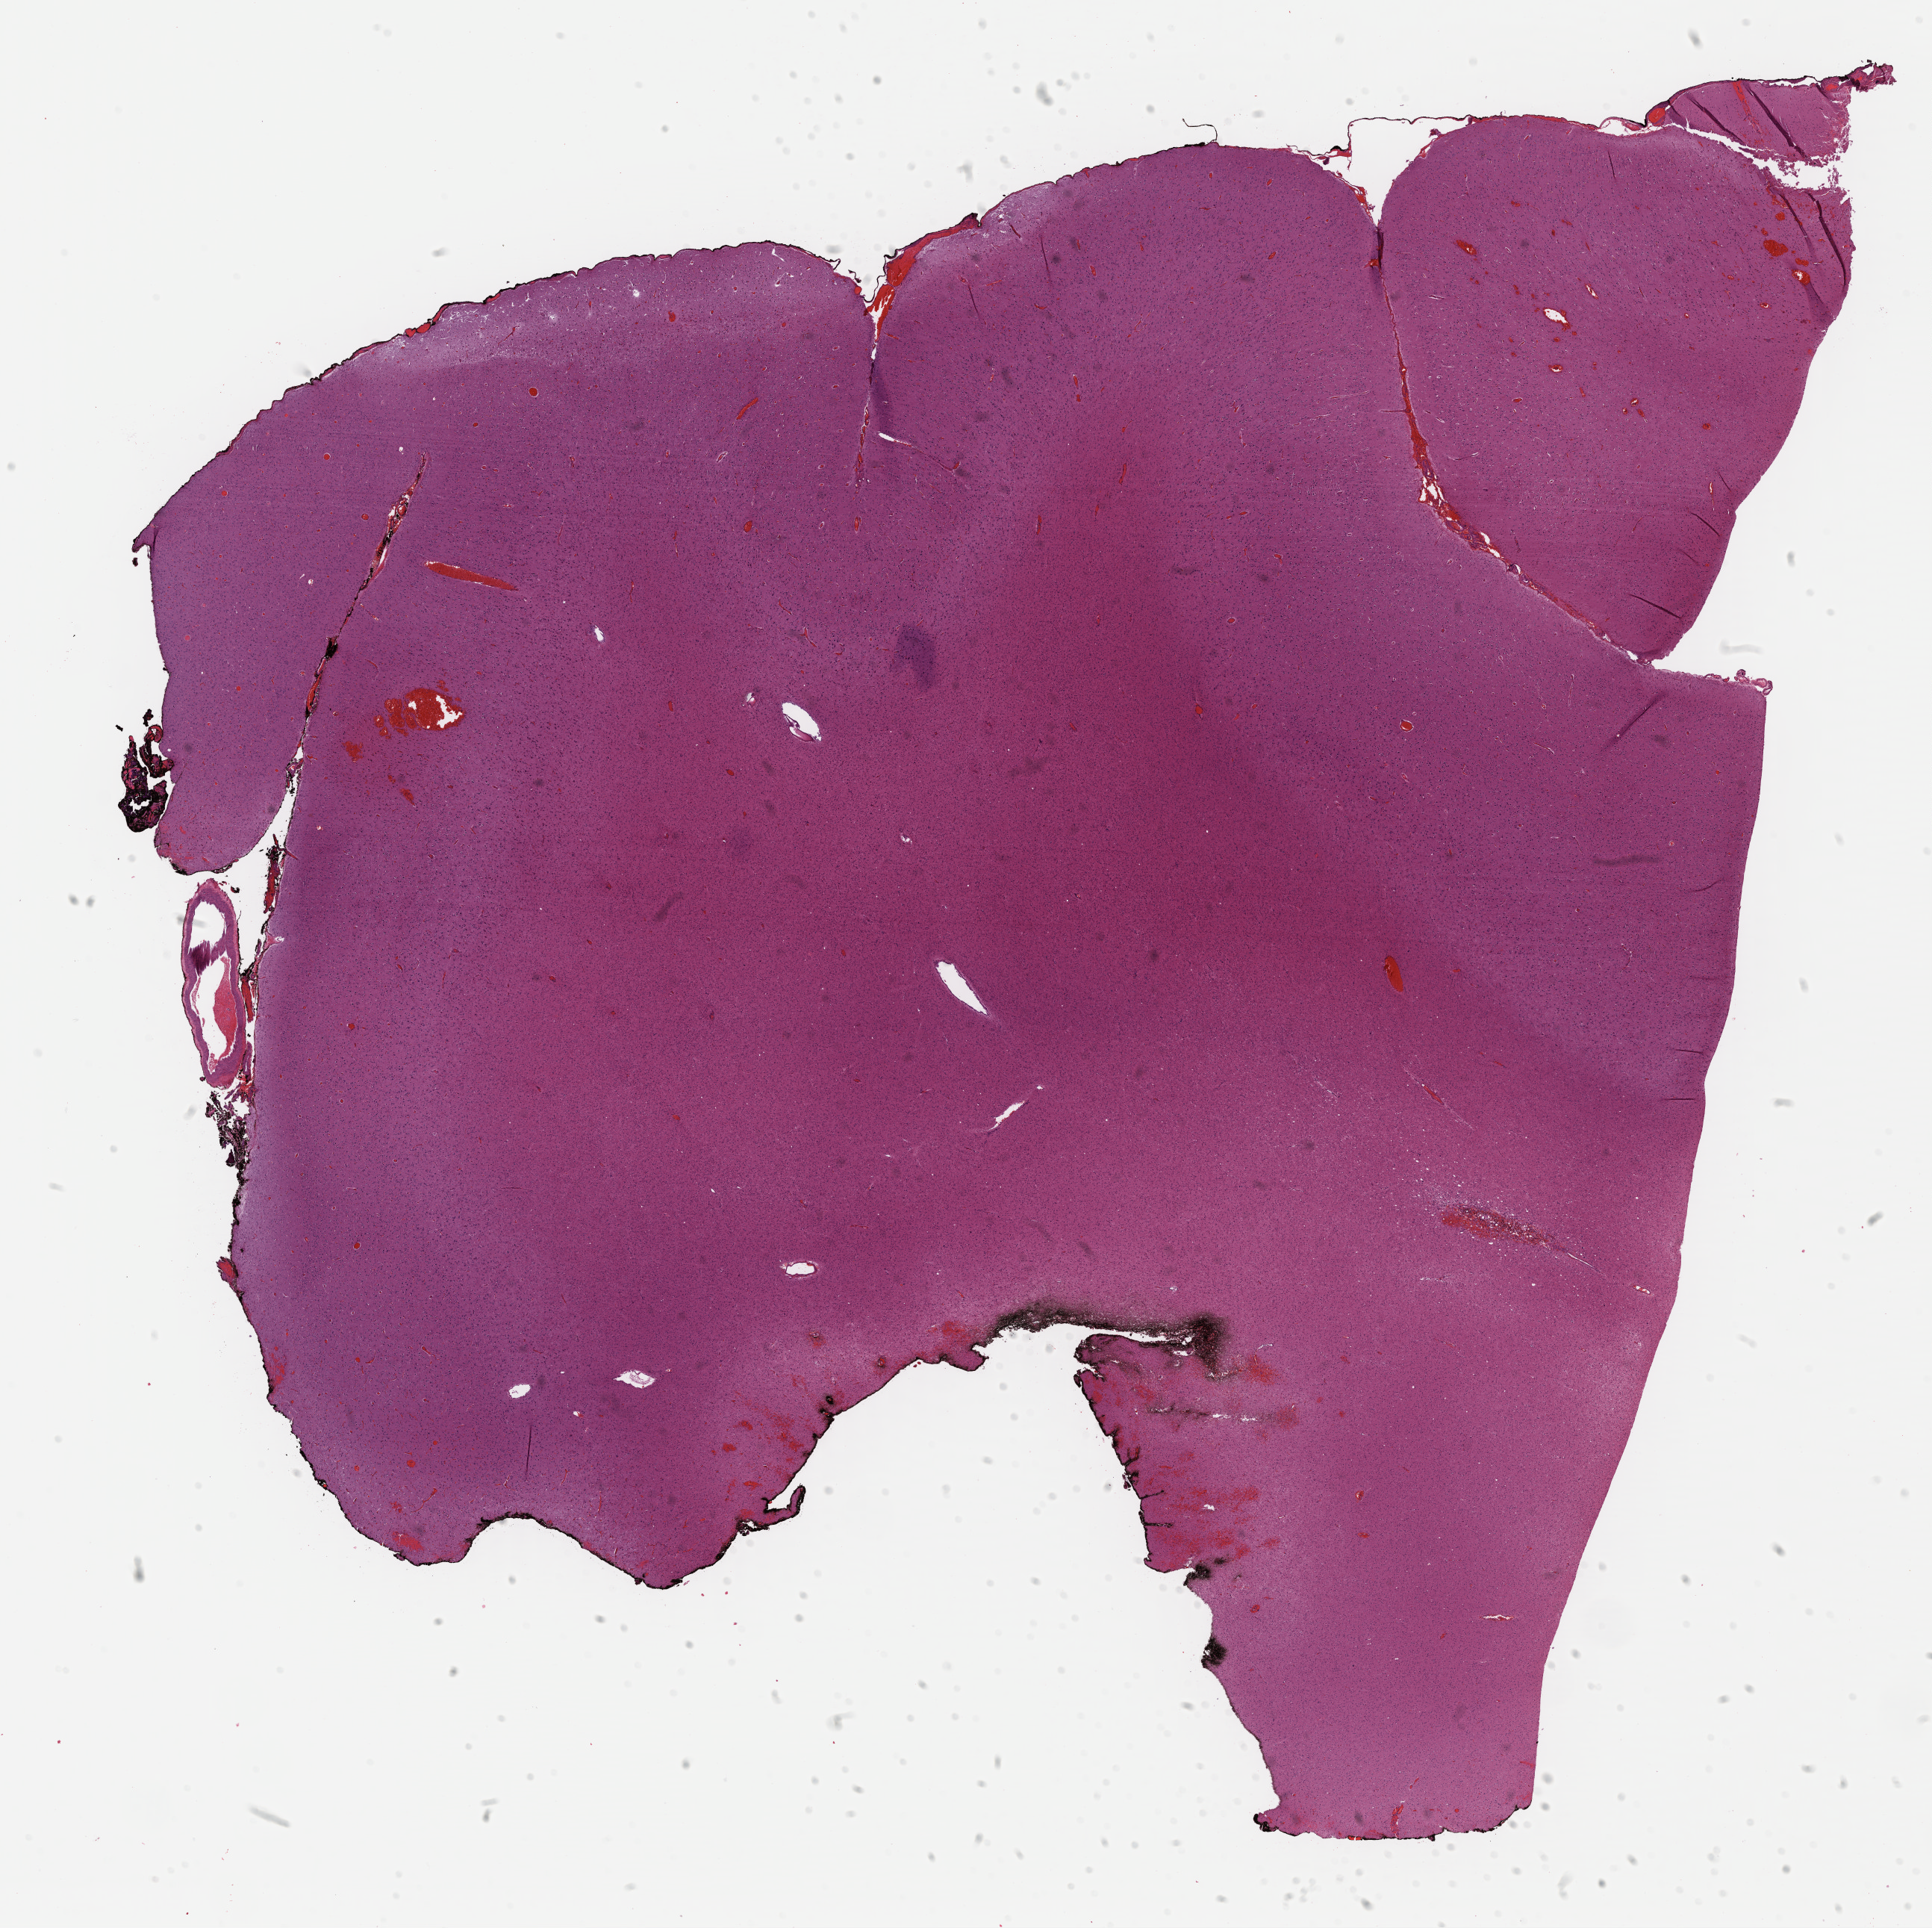
Whole-slide histology image, H&E, whole scanned area (about 20.3 x 20.3 mm) shown as a low-resolution overview, formalin-fixed paraffin-embedded (FFPE) diagnostic section, primary tumour sample from the brain. Female, age 61 years at initial diagnosis. Histologic grade: G2 (moderately differentiated).
Laterality: left. Pathologic diagnosis: Astrocytoma, NOS (cerebrum).